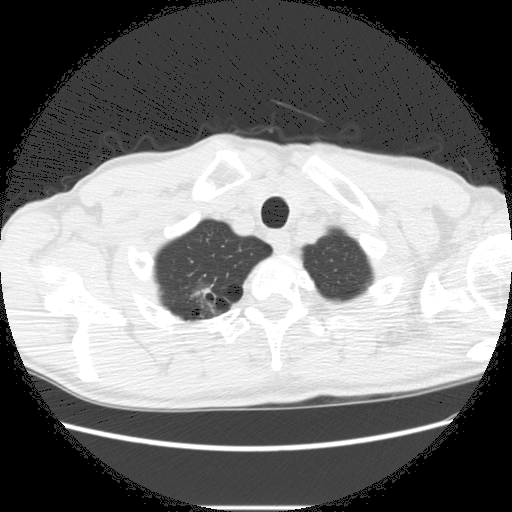
Low-dose screening chest CT, axial slice; second screening round (one year after baseline); lung window (W 1500 / L -600 HU); standard (soft-tissue) reconstruction kernel (STANDARD); slice 21 of 282 in the series. Male, age 66 years at enrolment.
Lesion marked by an expert reader, bounding box <170,275,235,327> (left, top, right, bottom; pixels). The screening reader recorded 5 non-calcified nodules or masses ≥4 mm on this exam; which of them this box marks is not recorded. Later outcome: lung cancer diagnosed 75 days after this screen — adenocarcinoma, NOS, right upper lobe, undifferentiated (G4), stage IA (AJCC 6th edition), 20 mm at pathology.